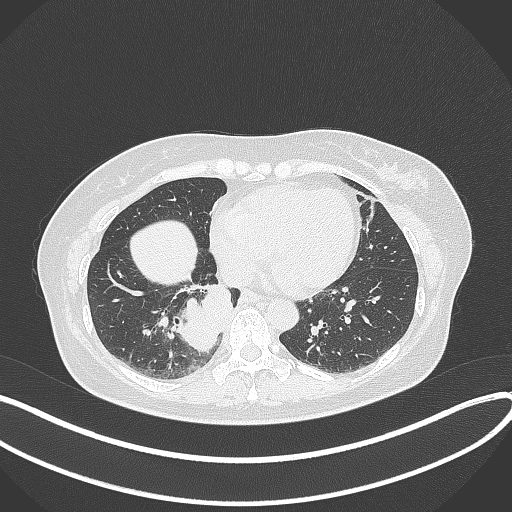
Chest CT, one axial slice; slice 119 of 331 in the series (ordered by position); reconstruction kernel B70f; 120 kVp; lung window (W 1500 / L -600 HU); 1 mm slice thickness; 512 × 512 image matrix. Patient: female, 54 years. Case-level facts recorded for this patient, not image findings: clinical TNM (as recorded): T4 N0 M0.
Annotated regions visible in this slice (bounding box drawn by a radiologist):
- lung tumour (recorded histology: adenocarcinoma): box from (x=166, y=278) to (x=235, y=357) px